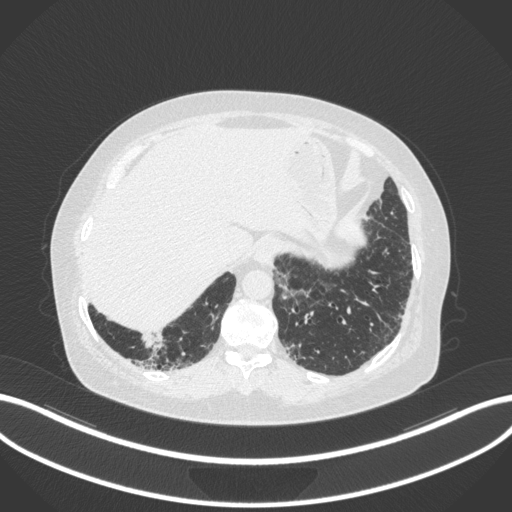
Chest CT, one axial slice; position 14 of 303 along the scan axis; reconstruction kernel B31f; 120 kVp; lung window (W 1500 / L -600 HU); 1 mm slice thickness; 512 × 512 image matrix. Female patient, age 65 years. From the clinical record (not read from this slice): clinical TNM (as recorded): T2b N1 M0.
Outlined on this slice (bounding box drawn by a radiologist):
- lung tumour (recorded histology: adenocarcinoma): box from (x=137, y=332) to (x=173, y=362) px